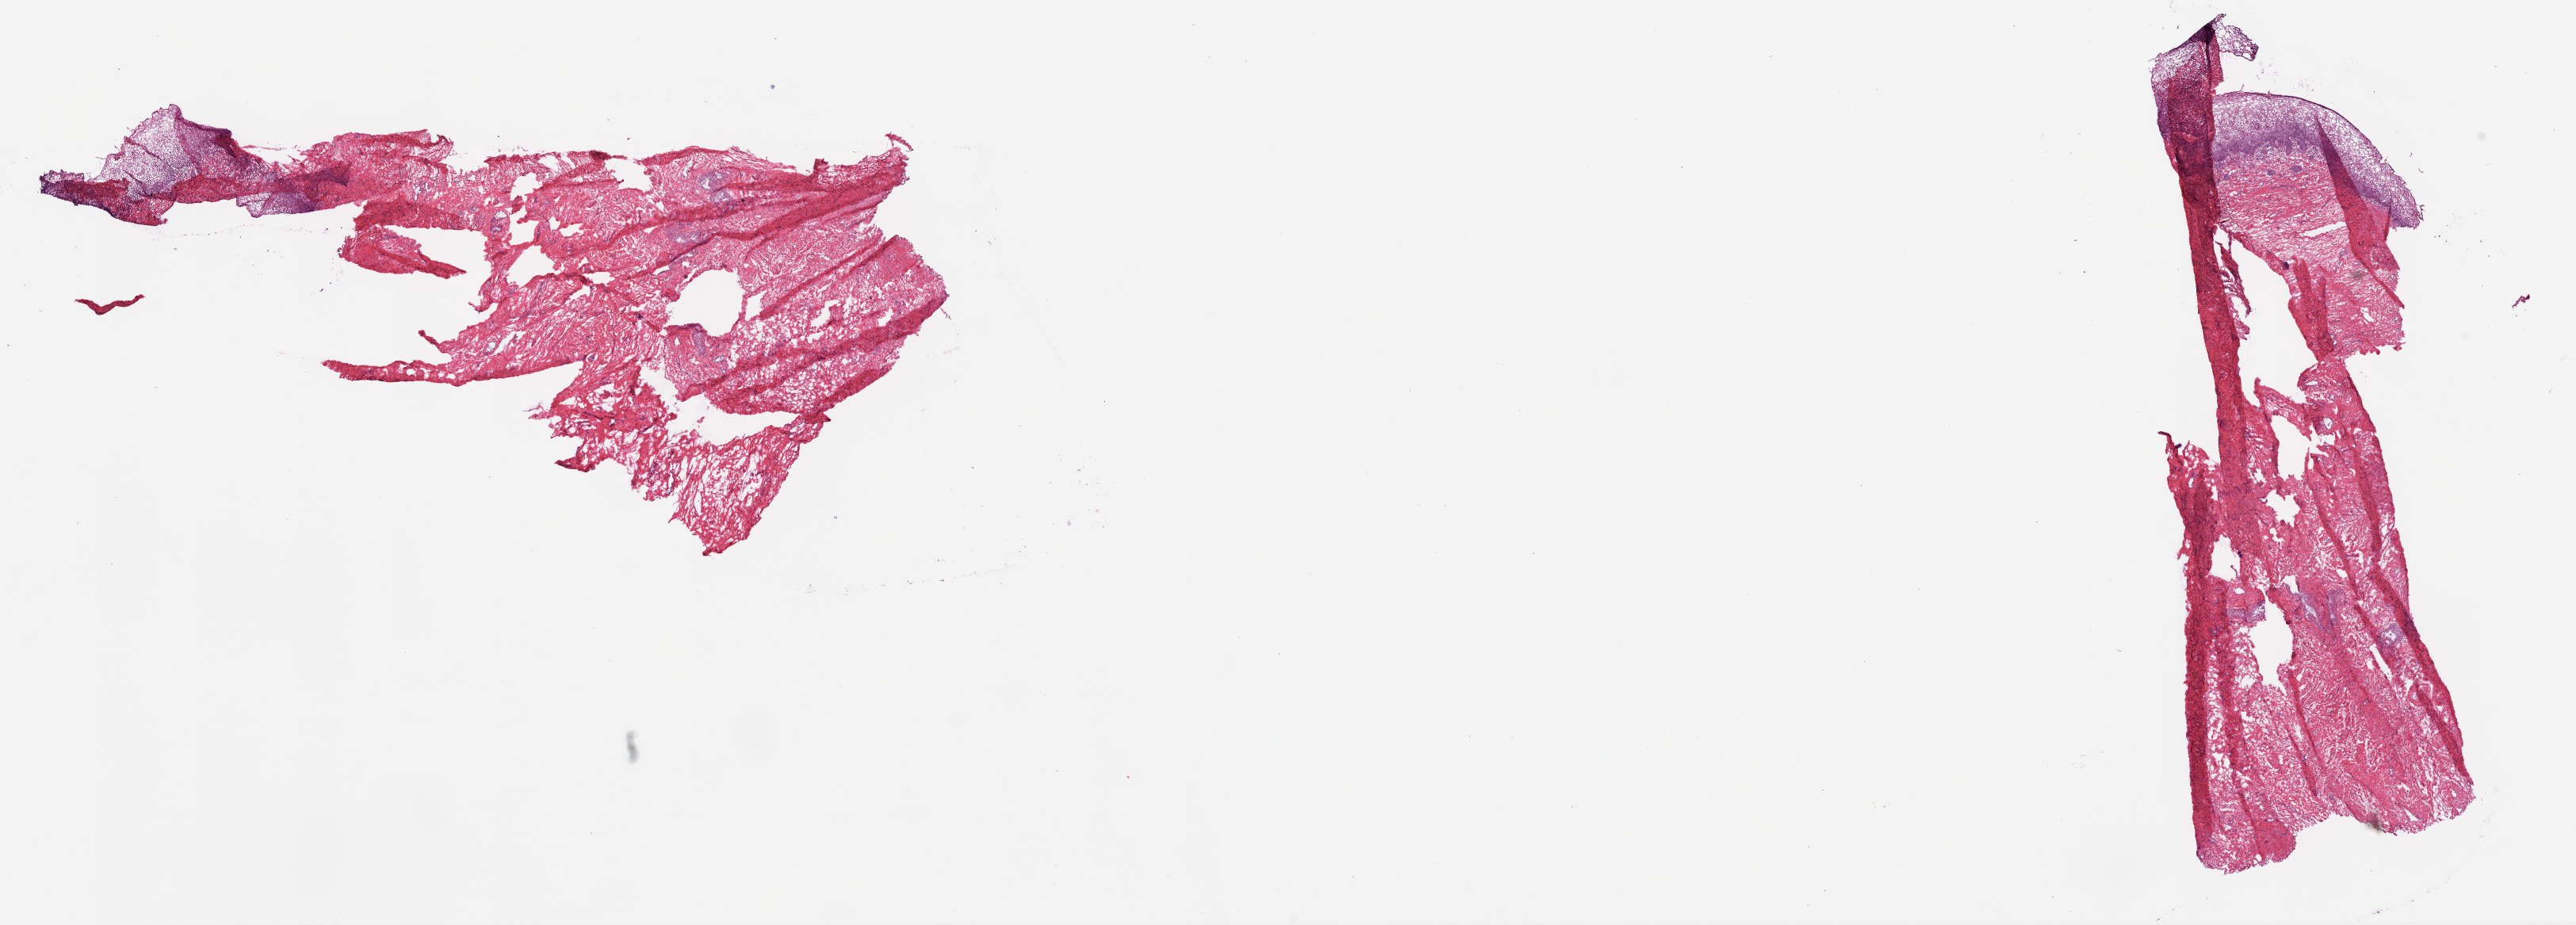
Digitized H&E tissue section (whole slide) — whole scanned area (about 26.1 x 9.4 mm, slide scanned at 20x) shown as a low-resolution overview; frozen section; sample: solid tissue normal (non-tumour tissue), ovary. Female, age 53 years at initial diagnosis.
This section: solid tissue normal (non-tumour) sample from the same patient. Patient diagnosis: Serous cystadenocarcinoma, NOS.